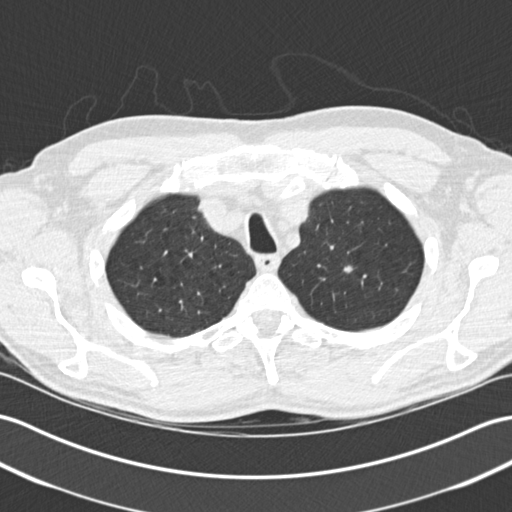
Low-dose screening chest CT, axial slice; first (baseline) screen; lung window (W 1500 / L -600 HU); standard (soft-tissue) reconstruction kernel (B30f); 120 kVp; slice 39 of 205 in the series; 512 × 512 image matrix. Male, age 64 years at enrolment. Former smoker at enrolment.
• Lesion marked by an expert reader, bounding box <329,255,364,286> (left, top, right, bottom; pixels).
• Reader record for this screening exam (exam-level; its link to the box is not recorded): non-calcified nodule or mass ≥4 mm, right upper lobe, 7 × 5 mm, spiculated (stellate) margins, soft tissue attenuation.
• Note: the box lies in the patient's left hemithorax on this image, whereas the reader's record names the right lung; they may be different findings.
• Official screen result: positive, change unspecified: nodule(s) >= 4 mm or enlarging nodule(s), mass(es), or other non-specific abnormalities suspicious for lung cancer.